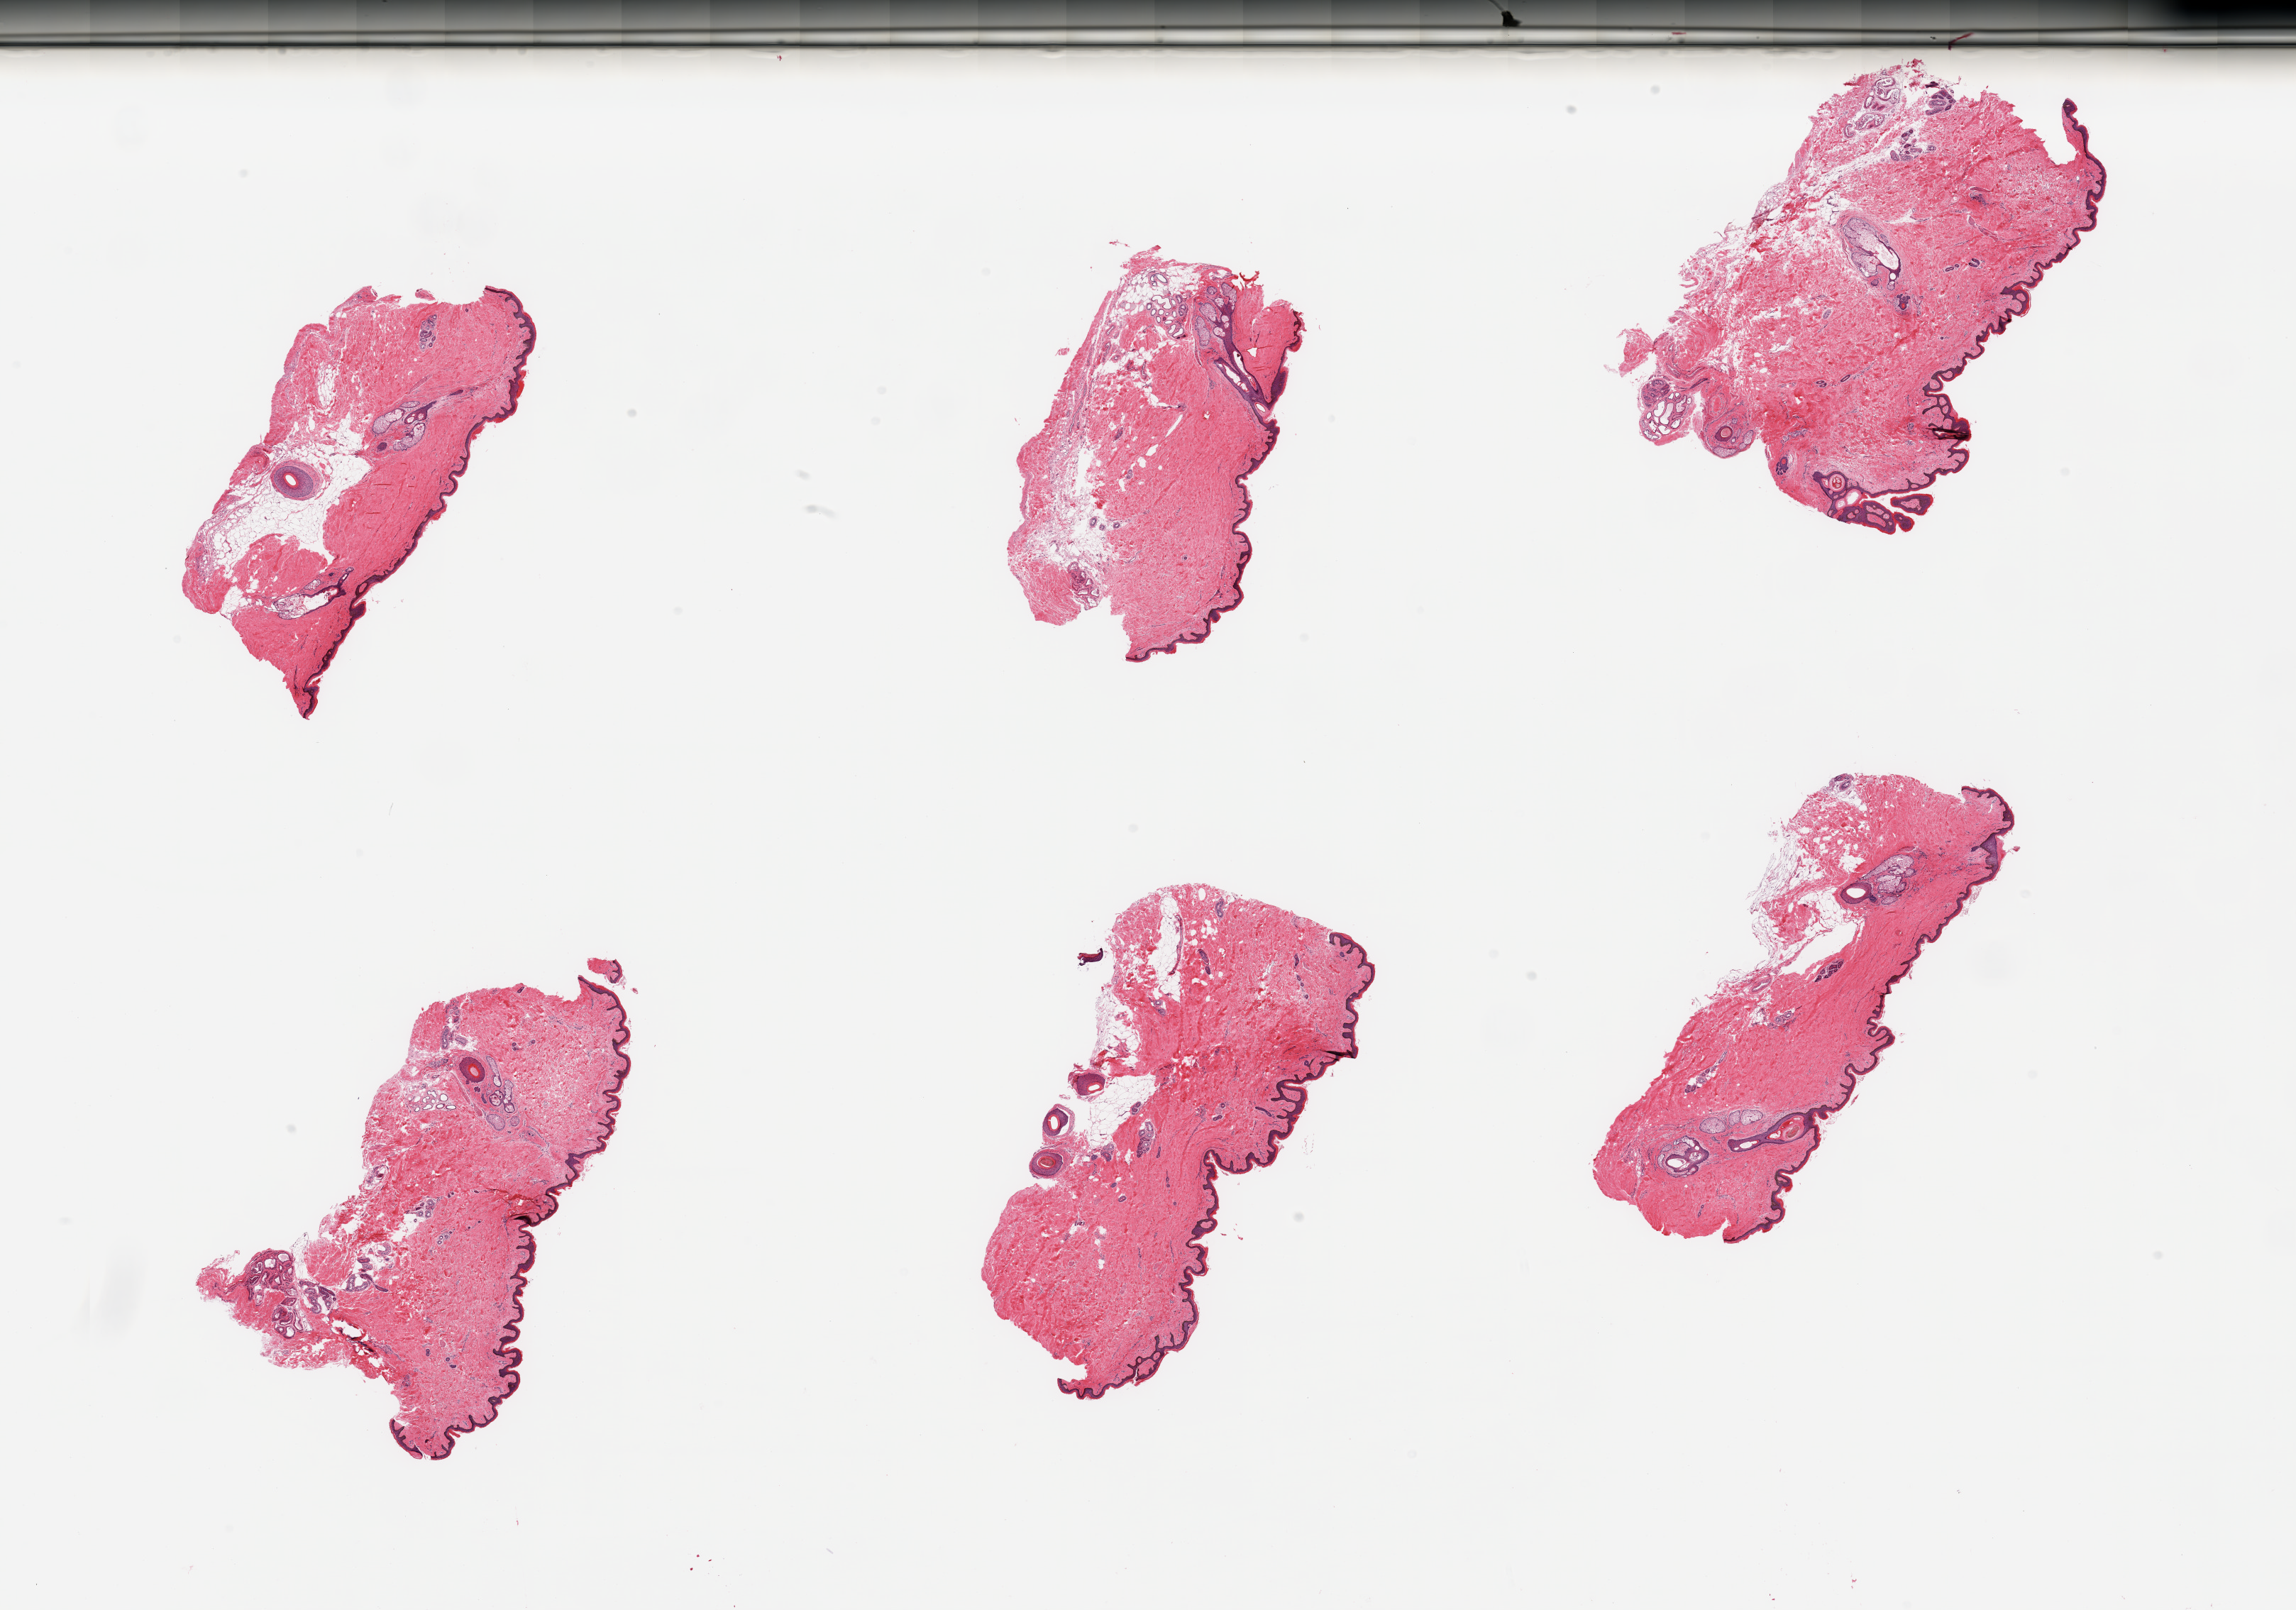
Digitized haematoxylin and eosin-stained section — a low-resolution overview of the entire scanned area, about 25.6 x 17.9 mm (slide scanned at 20x); PAXgene-fixed paraffin-embedded (PFPE) section; target tissue: skin of suprapubic region; donor tissue sample. Donor: male.
Reviewer comment on this tissue sample: 6 pieces, focal, minimal dermal fat; squamus epithelium is ~40 microns.